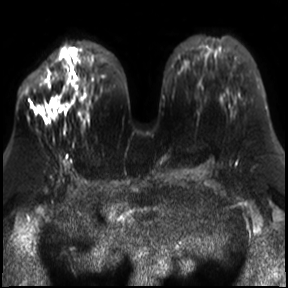
Breast MRI, one axial slice; position 15 of 30 along the scan axis; diffusion-weighted series; image 2 of 4 stored at this slice position (different b-values; order by instance number); 3 T; 4 mm slice thickness; 288 × 288 image matrix, field of view 340 × 340 mm. Female patient.
Outlined on this slice (expert manual segmentation):
- tumour on diffusion-weighted imaging: box from (x=35, y=97) to (x=59, y=119) px